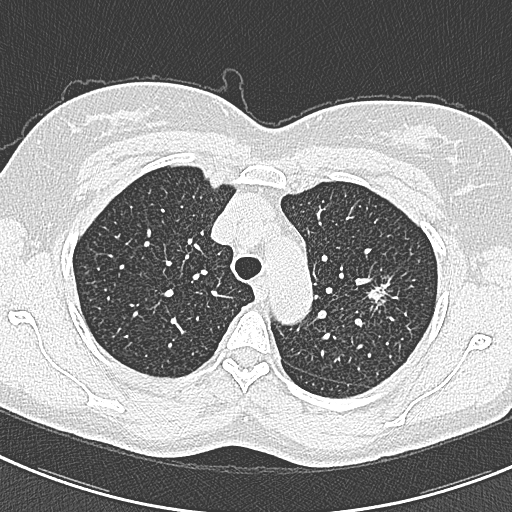
Chest CT (low-dose screening protocol), one axial image, baseline annual screen, lung window (W 1500 / L -600 HU), 120 kVp, slice 67 of 309 in the series. Female, age 57 years at enrolment. Current smoker at enrolment.
• Expert reader's lesion annotation, box from (x=362, y=271) to (x=412, y=323) px.
• The screening reader recorded 2 non-calcified nodules or masses ≥4 mm on this exam; which of them this box marks is not recorded.
• Lung cancer was diagnosed 198 days after this screen: adenocarcinoma, NOS, left upper lobe, well differentiated (G1), stage IA (AJCC 6th edition), 10 mm at pathology.